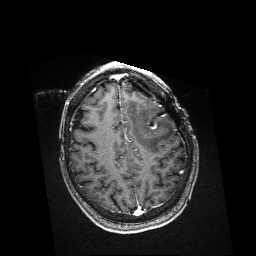
Brain MRI from a brain-tumour surgery series, one axial slice; T1-weighted post-contrast; 256 × 256 image matrix. Case-level facts recorded for this patient, not image findings: histopathology: Metastatic Melanoma.
Structures marked on this image (expert manual segmentation):
- residual tumour: box from (x=150, y=123) to (x=156, y=130) px